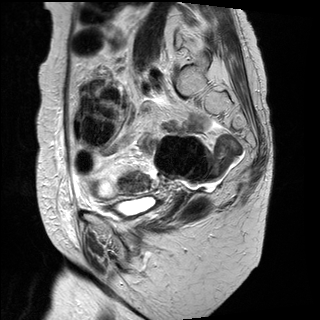
Pelvic MRI for cervical cancer, one sagittal slice; slice 21 of 31 in the series (ordered by position); T2-weighted; 1.5 T; TE 89 ms, TR 3890 ms; 4 mm slice thickness; 320 × 320 image matrix, field of view 260 × 260 mm. Female patient, age 61 years.
Outlined on this slice (manually delineated by an expert):
- uterus and cervix: bounding box [x1, y1, x2, y2] px = [119, 170, 150, 193]